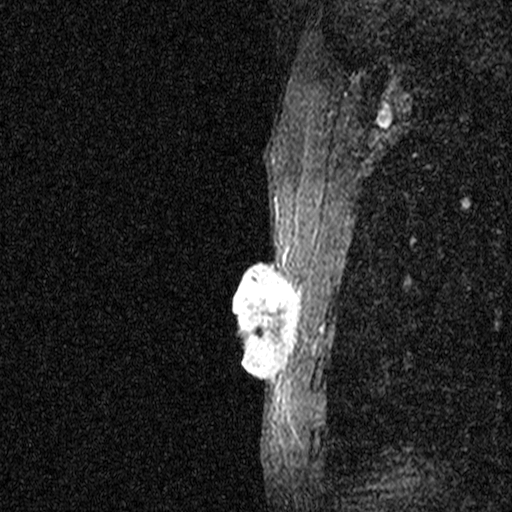
Breast MRI (dynamic contrast-enhanced), one sagittal slice. Position 37 of 44 along the scan axis. Dynamic contrast-enhanced study with each time point stored as its own series, time point 2 of 3 at this slice position (early post-contrast, ordered by acquisition time). 1.5 T. TE 4.5 ms, TR 11 ms. 2.05 mm slice thickness. 512 × 512 image matrix, field of view 200 × 200 mm. Female patient, age 44 years. From the clinical record (not read from this slice): setting: breast cancer imaged before/during neoadjuvant chemotherapy; receptor status: HR-positive, HER2-negative.
Annotated regions visible in this slice (semi-automatically segmented with operator editing):
- analysis volume of interest (the breast-tissue region the enhancement analysis was run in; not a lesion): box from (x=204, y=254) to (x=312, y=401) px
- tumour enhancement mask (voxels above the 90 % enhancement threshold inside the analysis volume of interest): (x=234, y=255)–(x=300, y=401)